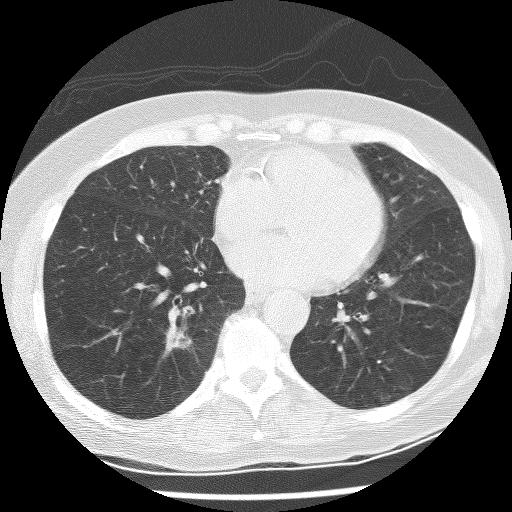
Low-dose screening chest CT, one axial slice. Position 99 of 247 along the scan axis. Reconstruction kernel BONE. Lung window (W 1500 / L -600 HU). 2.5 mm slice thickness. 512 × 512 image matrix.
Annotated regions visible in this slice (expert manual segmentation):
- lesion 1 (tumor, lower lobe of right lung): bounding box [x1, y1, x2, y2] px = [162, 326, 193, 358]